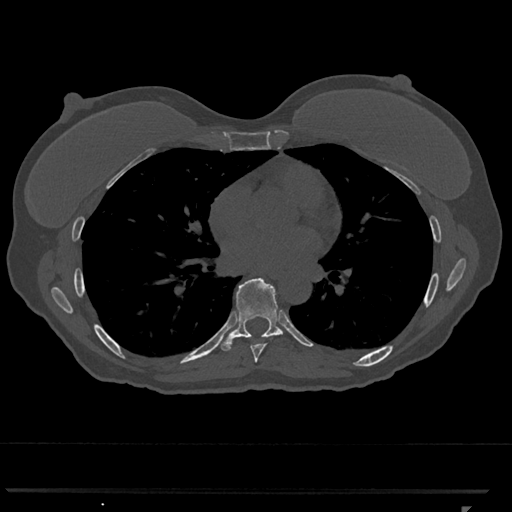
CT including the spine, one axial slice; slice 685 of 793 in the series (ordered by position); reconstruction kernel Br40s/3; 120 kVp; bone window (W 1800 / L 400 HU); 0.5 mm slice thickness; 512 × 512 image matrix, field of view 380 × 380 mm. Patient: female, 62 years. From the clinical record (not read from this slice): primary cancer: renal.
Annotated regions visible in this slice (semi-automatic segmentation, software-assisted and operator-edited):
- T7 vertebra: bounding box (x1, y1, x2, y2) in pixels: (249, 337, 265, 363)
- T8 vertebra: (219, 278, 283, 351)